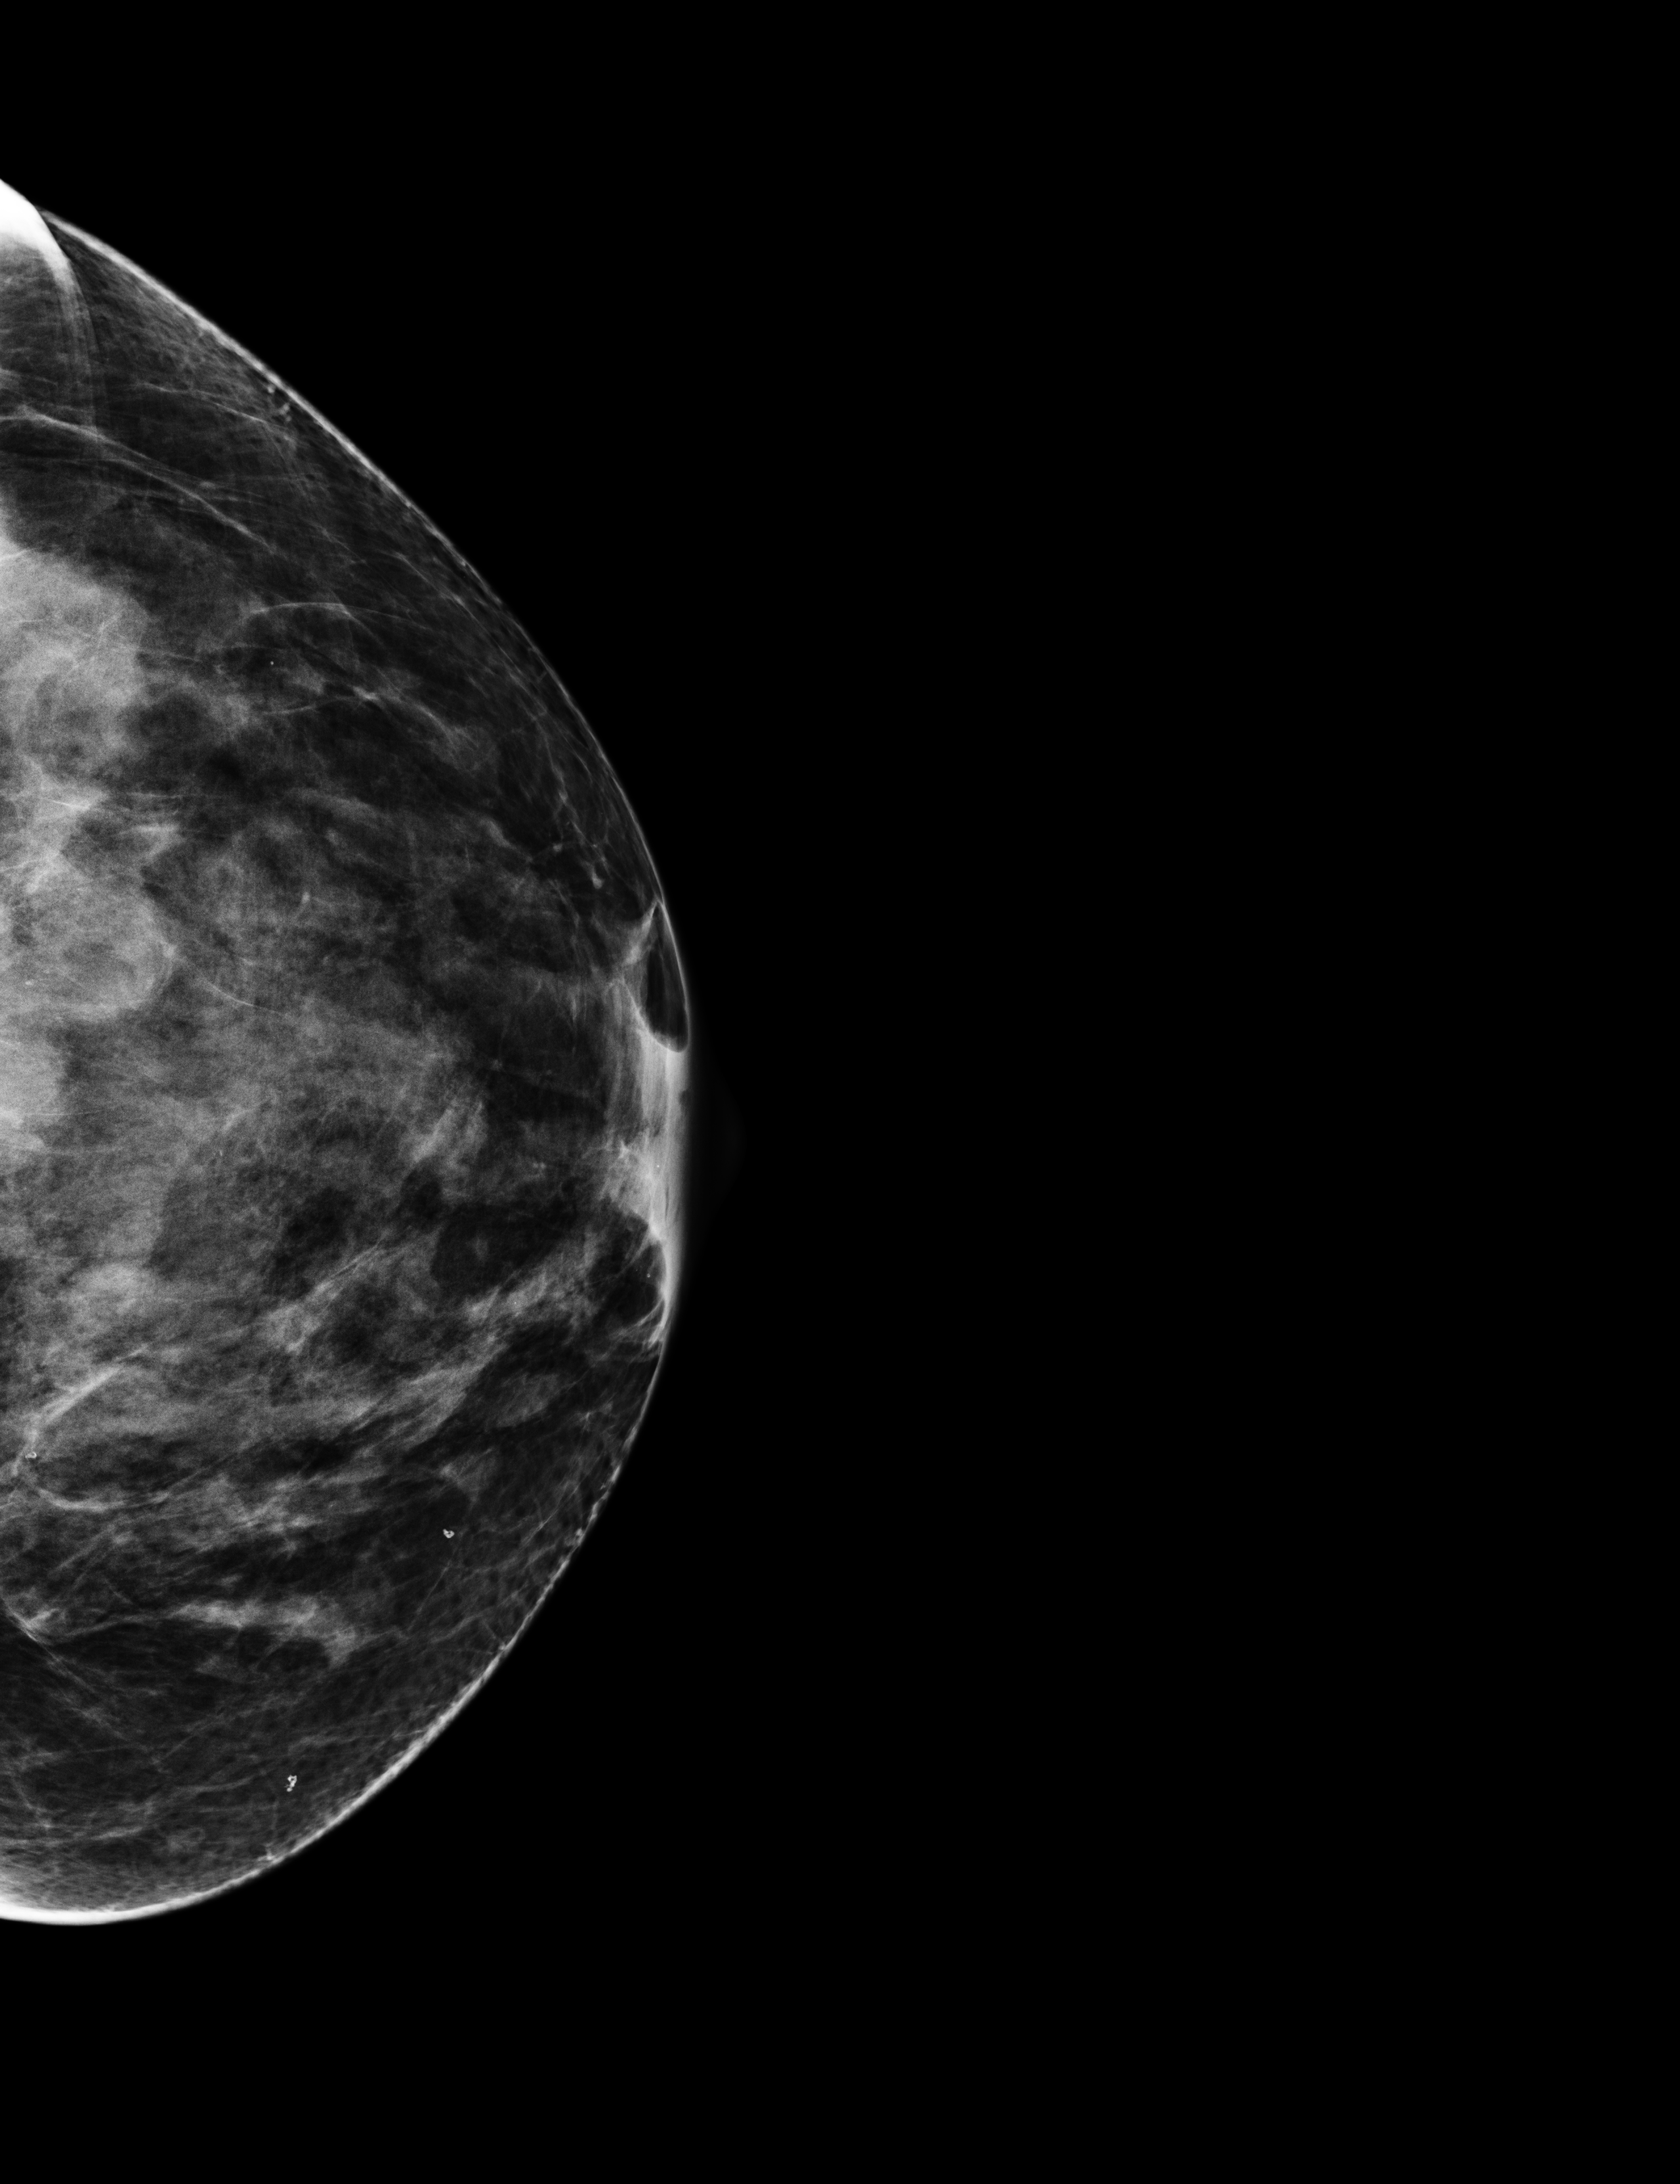
Annual screening mammography examination; system: Selenia Dimensions. Patient: female, 64 years.
Image type: full-field digital mammogram. Breast: left. Projection: CC view.